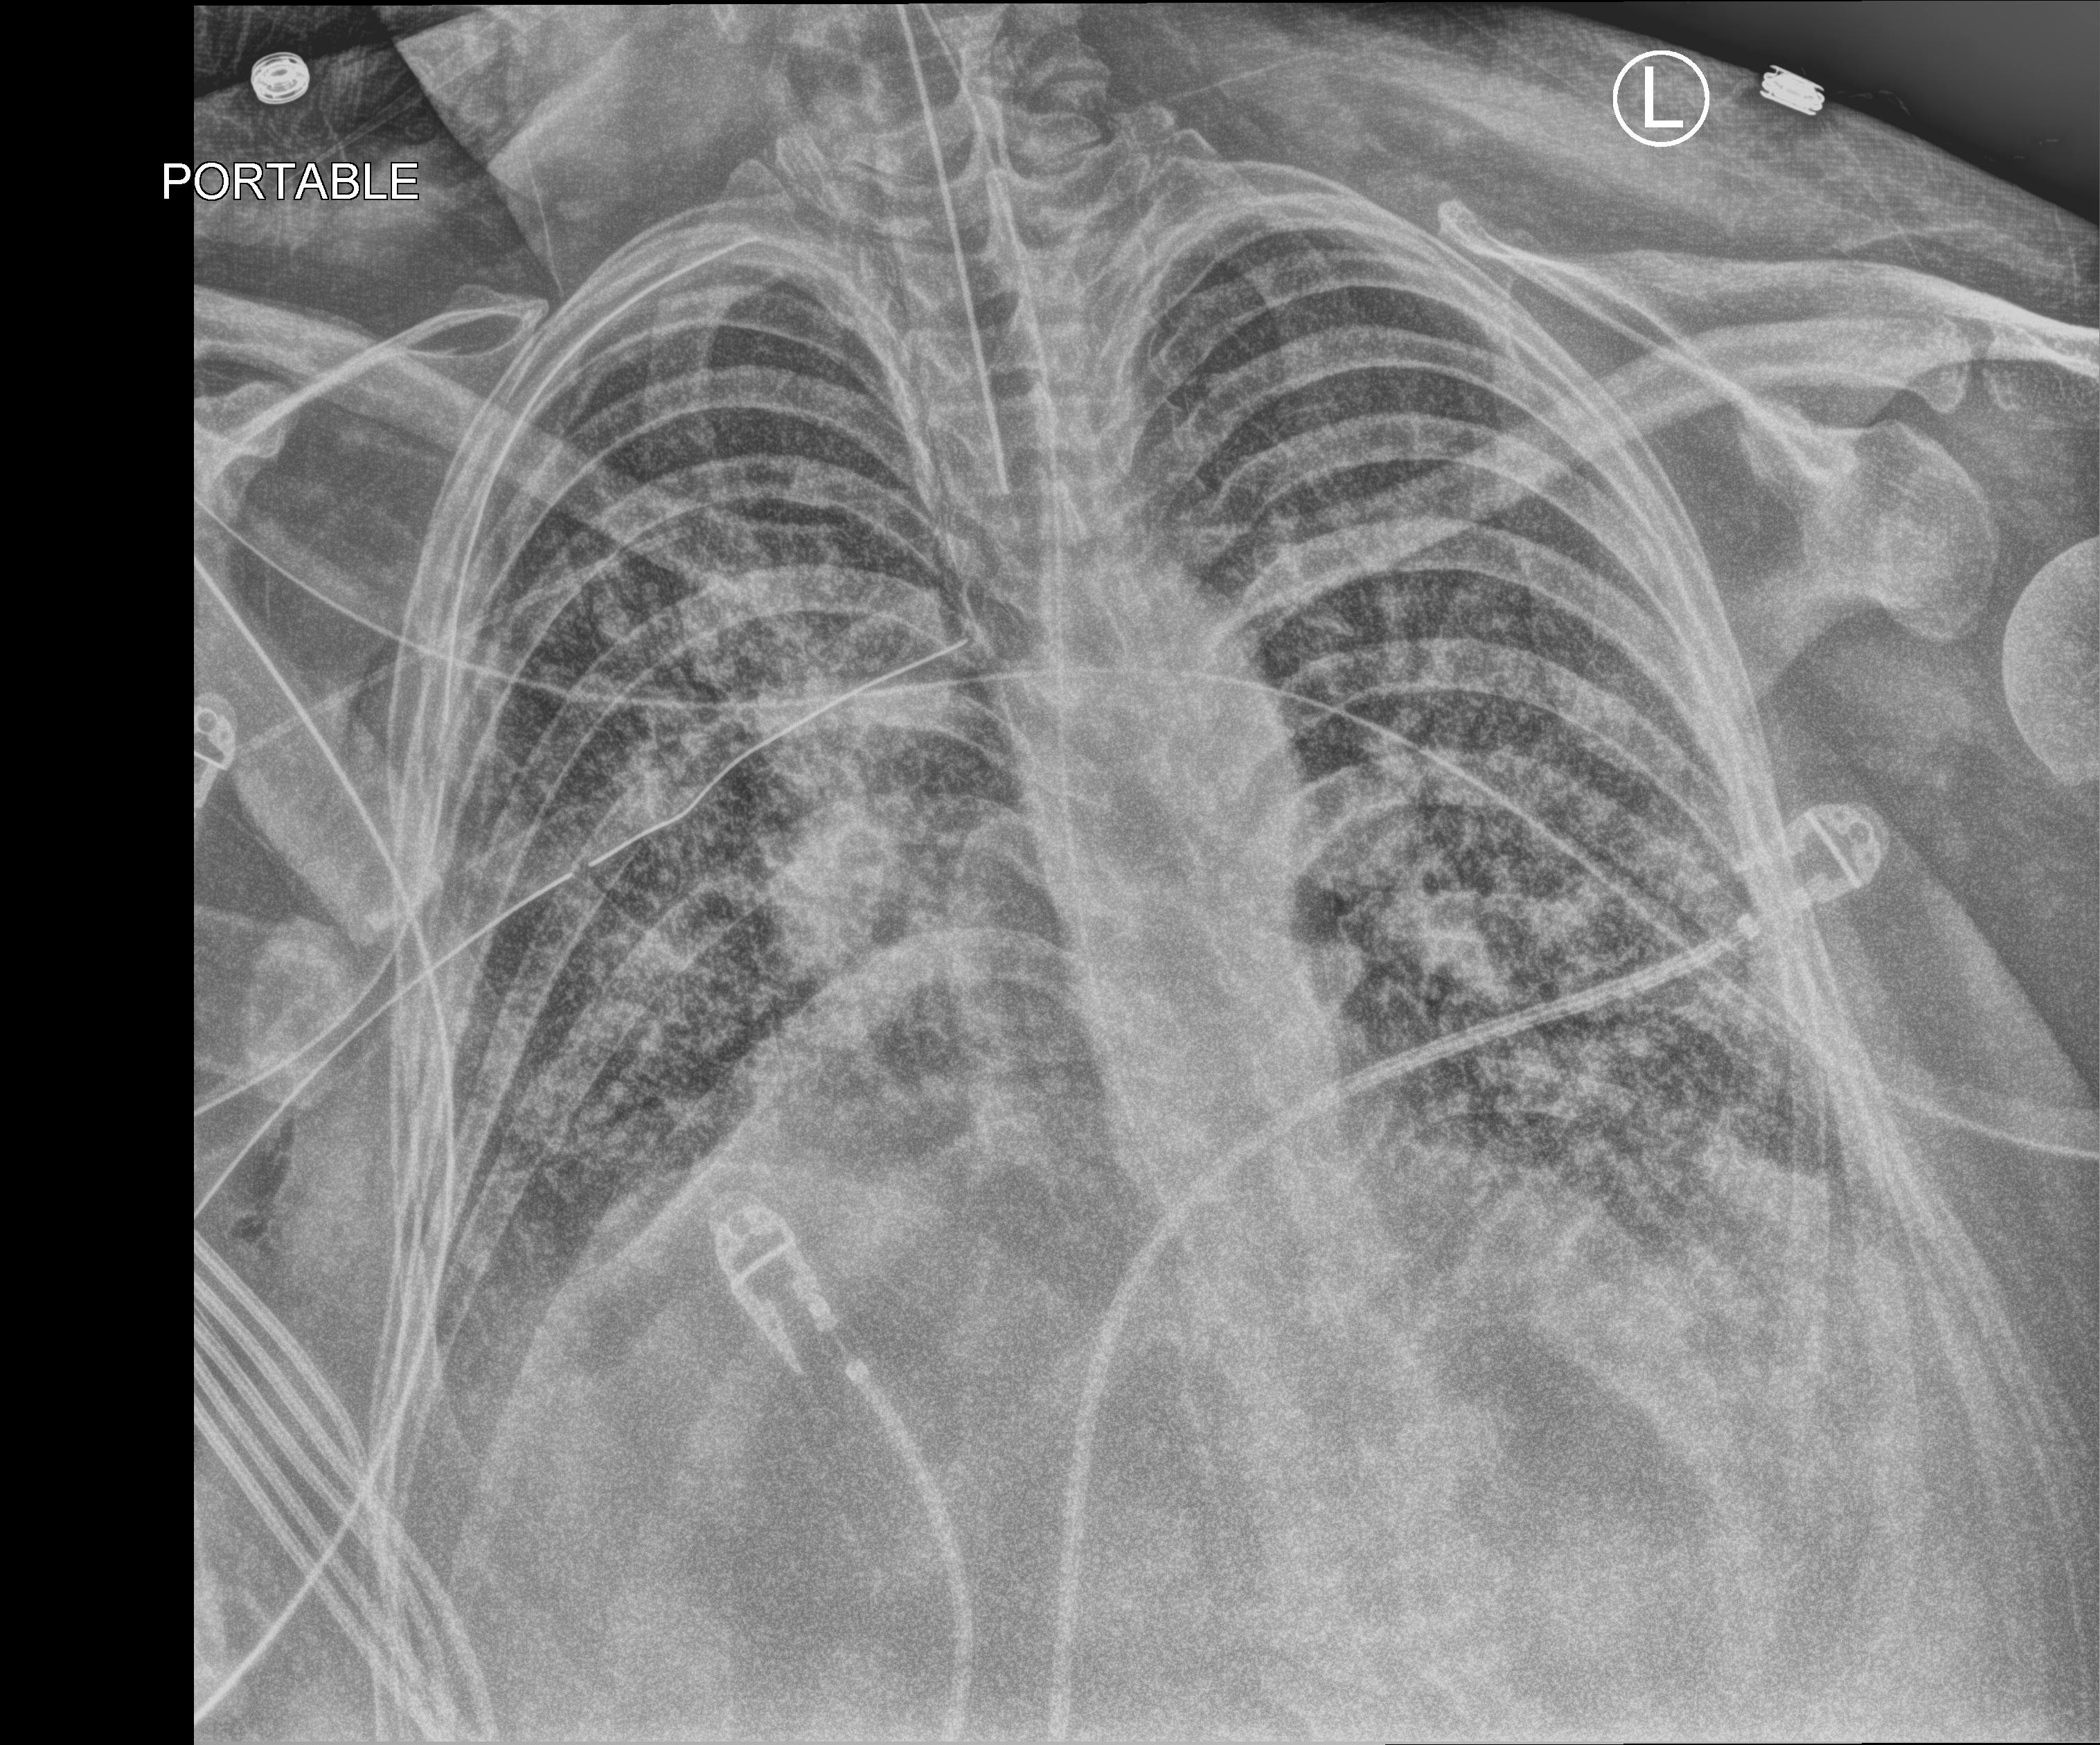
Bedside chest radiograph (computed radiography), anteroposterior (AP) projection. Adult patient hospitalised with COVID-19, age 18–59 years.
Hospital-stay facts (about this admission, not read from this image; timing relative to this image not recorded): admitted to intensive care during this hospital stay: yes; mechanically ventilated during this hospital stay: yes; length of hospital stay: 48 days.